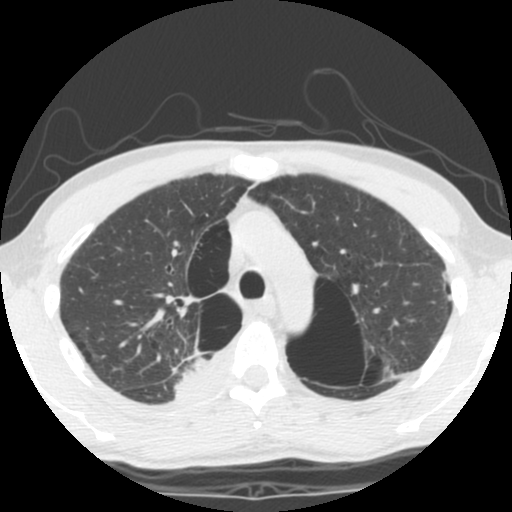
Low-dose screening chest CT, one axial slice; position 85 of 119 along the scan axis; reconstruction kernel STANDARD; 140 kVp; lung window (W 1500 / L -600 HU); 2.5 mm slice thickness; 512 × 512 image matrix, field of view 295 × 295 mm.
Annotated regions visible in this slice (expert manual segmentation):
- lesion 1 (tumor, upper lobe of right lung): box from (x=176, y=354) to (x=231, y=401) px